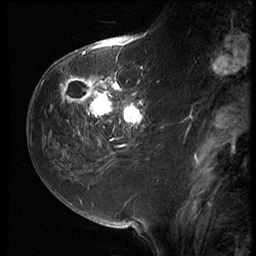
Breast MRI (dynamic contrast-enhanced), one sagittal slice. Position 26 of 64 along the scan axis. 3 images stored at this slice position (order not interpretable as contrast timing). 1.5 T. TE 4.2 ms, TR 9 ms. 256 × 256 image matrix, field of view 180 × 180 mm. Female patient, age 59 years. From the clinical record (not read from this slice): setting: breast cancer imaged before/during neoadjuvant chemotherapy; receptor status: HER2-positive.
Structures marked on this image (semi-automatic segmentation, software-assisted and operator-edited):
- analysis volume of interest (the breast-tissue region the enhancement analysis was run in; not a lesion): box from (x=54, y=65) to (x=155, y=132) px
- tumour enhancement mask (voxels above the 140 % enhancement threshold inside the analysis volume of interest): (x=61, y=67)–(x=146, y=130)